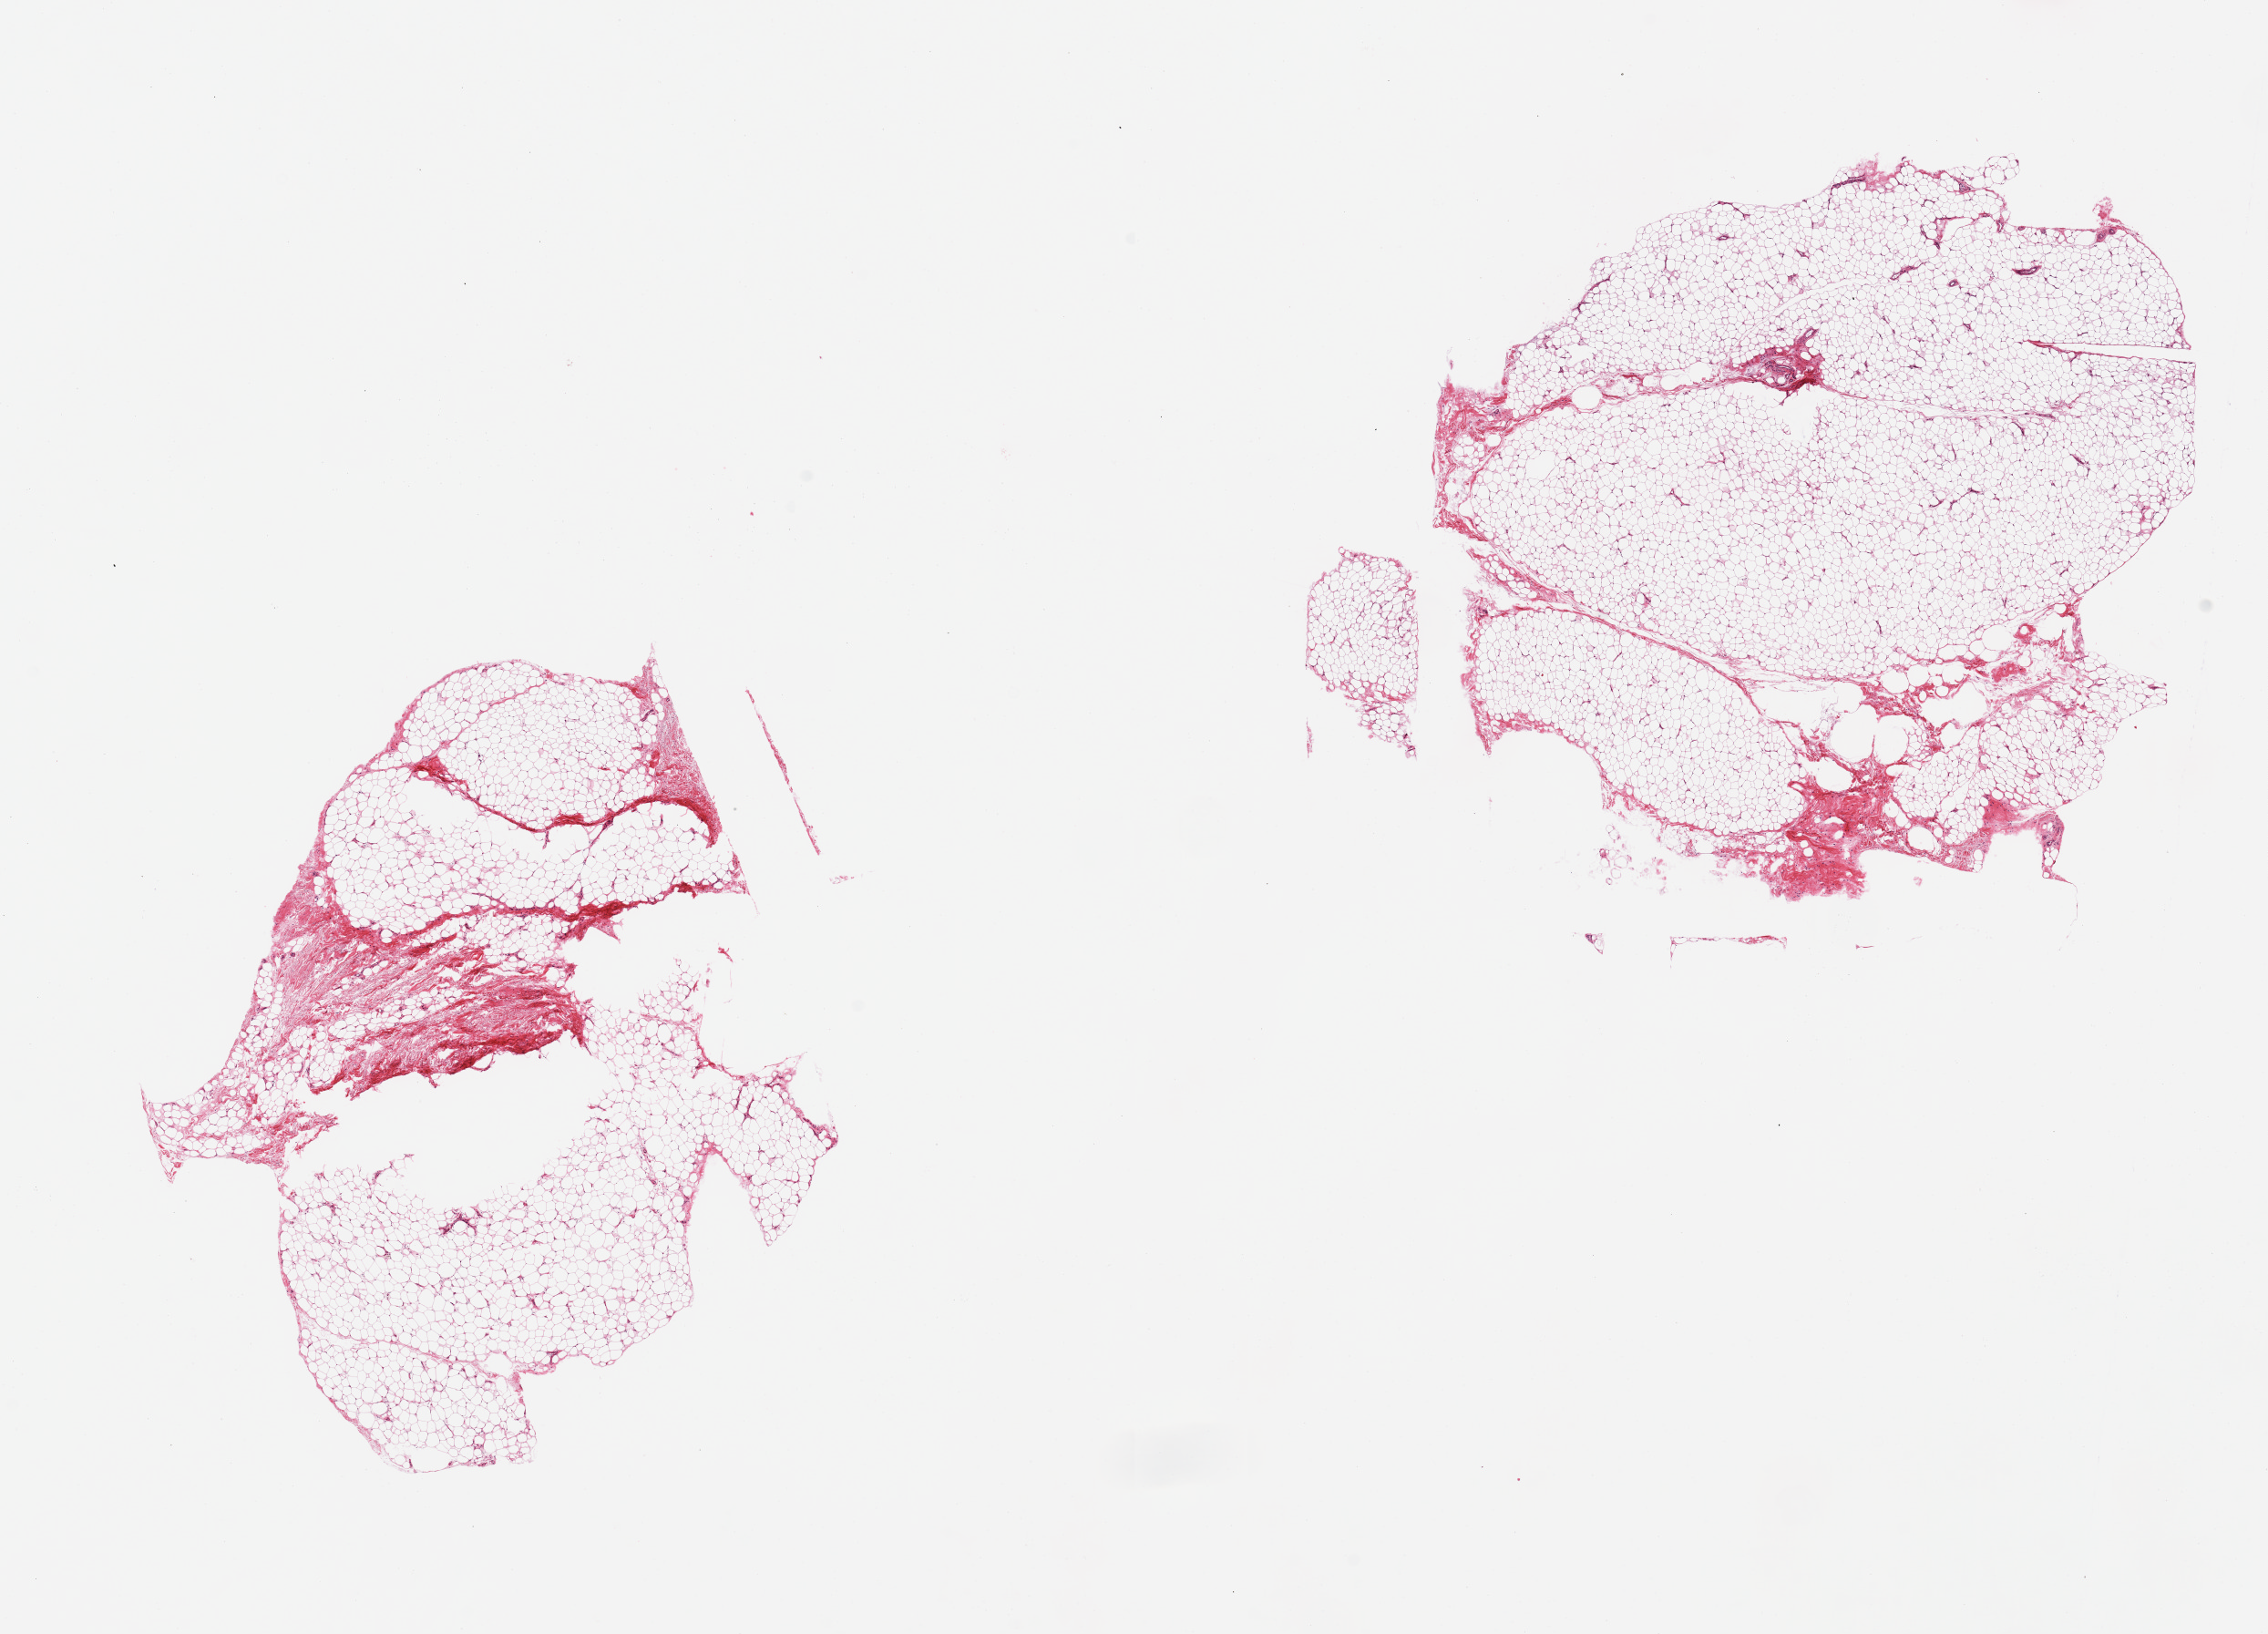
Whole-slide image, H&E stain — low-resolution overview of the scanned area, about 19.7 x 14.2 mm (slide scanned at 20x), PAXgene-fixed paraffin-embedded (PFPE) section, sampled site (target tissue): adipose tissue, tissue donor sample. Donor: female.
Pathologist's review note for this sample: 3 pieces; ~1--15% fibrofascial tissue or vascular elements.